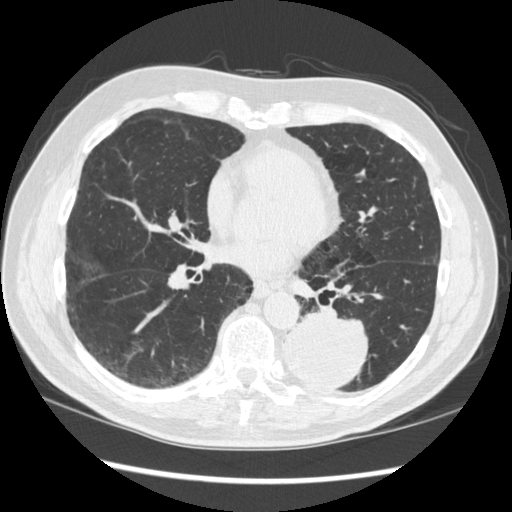
Axial slice from a low-dose chest CT screening exam. First (baseline) screen. Lung window (W 1500 / L -600 HU). 1.25 mm slice thickness. Standard (soft-tissue) reconstruction kernel (STANDARD). 120 kVp. Male, age 72 years at enrolment.
Expert reader's lesion annotation, box from (x=268, y=302) to (x=372, y=393) px. The screening reader recorded 2 non-calcified nodules or masses ≥4 mm on this exam (left lower lobe, right middle lobe); which of them this box marks is not recorded. Lung cancer was diagnosed 37 days after this screen: squamous cell carcinoma, NOS, left lower lobe, stage IIIA (AJCC 6th edition), 60 mm at pathology.